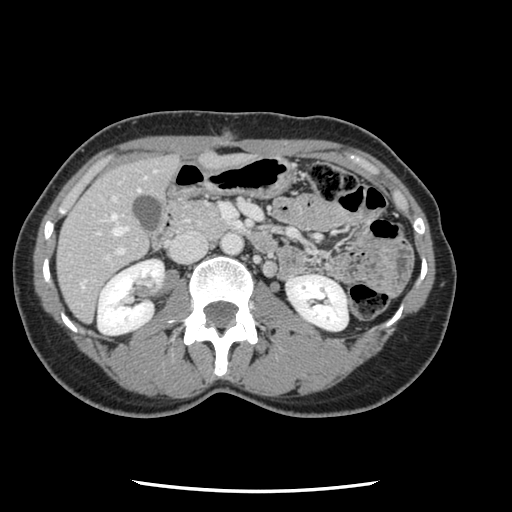
Contrast-enhanced abdominal CT, one axial slice. Position 42 of 134 along the scan axis. 120 kVp. Intravenous contrast given. Soft-tissue window (W 400 / L 40 HU). 512 × 512 image matrix. Female patient, age 43 years. Case-level facts recorded for this patient, not image findings: diagnosis: colorectal cancer liver metastases, imaged before liver resection; multiple liver metastases: yes; largest metastasis: 3.4 cm; disease in both lobes: yes.
Annotated regions visible in this slice (expert manual segmentation):
- hepatic veins: bounding box [x1, y1, x2, y2] px = [81, 190, 140, 288]
- liver: [58, 156, 179, 320]
- planned liver remnant (the part of the liver to remain after resection): [58, 156, 178, 321]
- portal vein (with intrahepatic branches): [95, 202, 261, 262]